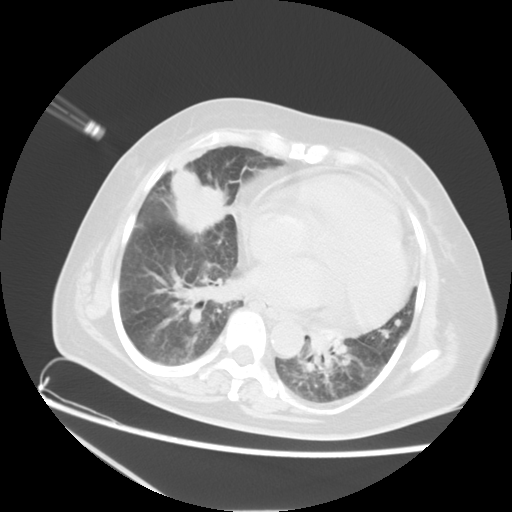
Chest CT, one axial slice; position 7 of 21 along the scan axis; reconstruction kernel STANDARD; 120 kVp; lung window (W 1500 / L -600 HU); 5 mm slice thickness; 512 × 512 image matrix, field of view 350 × 350 mm. Female patient, age 67 years. Case-level facts recorded for this patient, not image findings: clinical TNM (as recorded): T2a N3 M1a.
Structures marked on this image (bounding box drawn by a radiologist):
- lung tumour (recorded histology: adenocarcinoma): bounding box (x1, y1, x2, y2) in pixels: (169, 160, 227, 237)